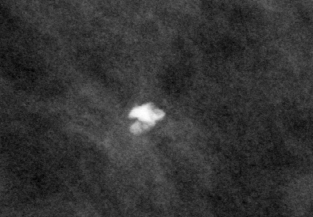
Region of interest cut from a scanned film mammogram (one marked finding); left breast; MLO view; BI-RADS breast density category 1 (scale 1–4).
Finding: calcifications, morphology coarse; BI-RADS assessment category 2; benign; no additional work-up was recommended (benign without callback).